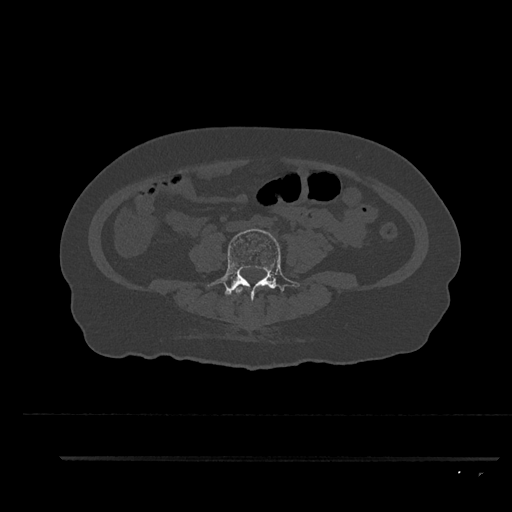
CT including the spine, one axial slice; slice 31 of 797 in the series (ordered by position); reconstruction kernel Br40s/3; 120 kVp; bone window (W 1800 / L 400 HU); 0.5 mm slice thickness; 512 × 512 image matrix, field of view 408 × 408 mm. Female patient, age 44 years. Case-level facts recorded for this patient, not image findings: primary cancer: renal.
Structures marked on this image (semi-automatic segmentation, software-assisted and operator-edited):
- L3 vertebra: box from (x=235, y=286) to (x=243, y=294) px
- L4 vertebra: (x=207, y=229)–(x=300, y=304)